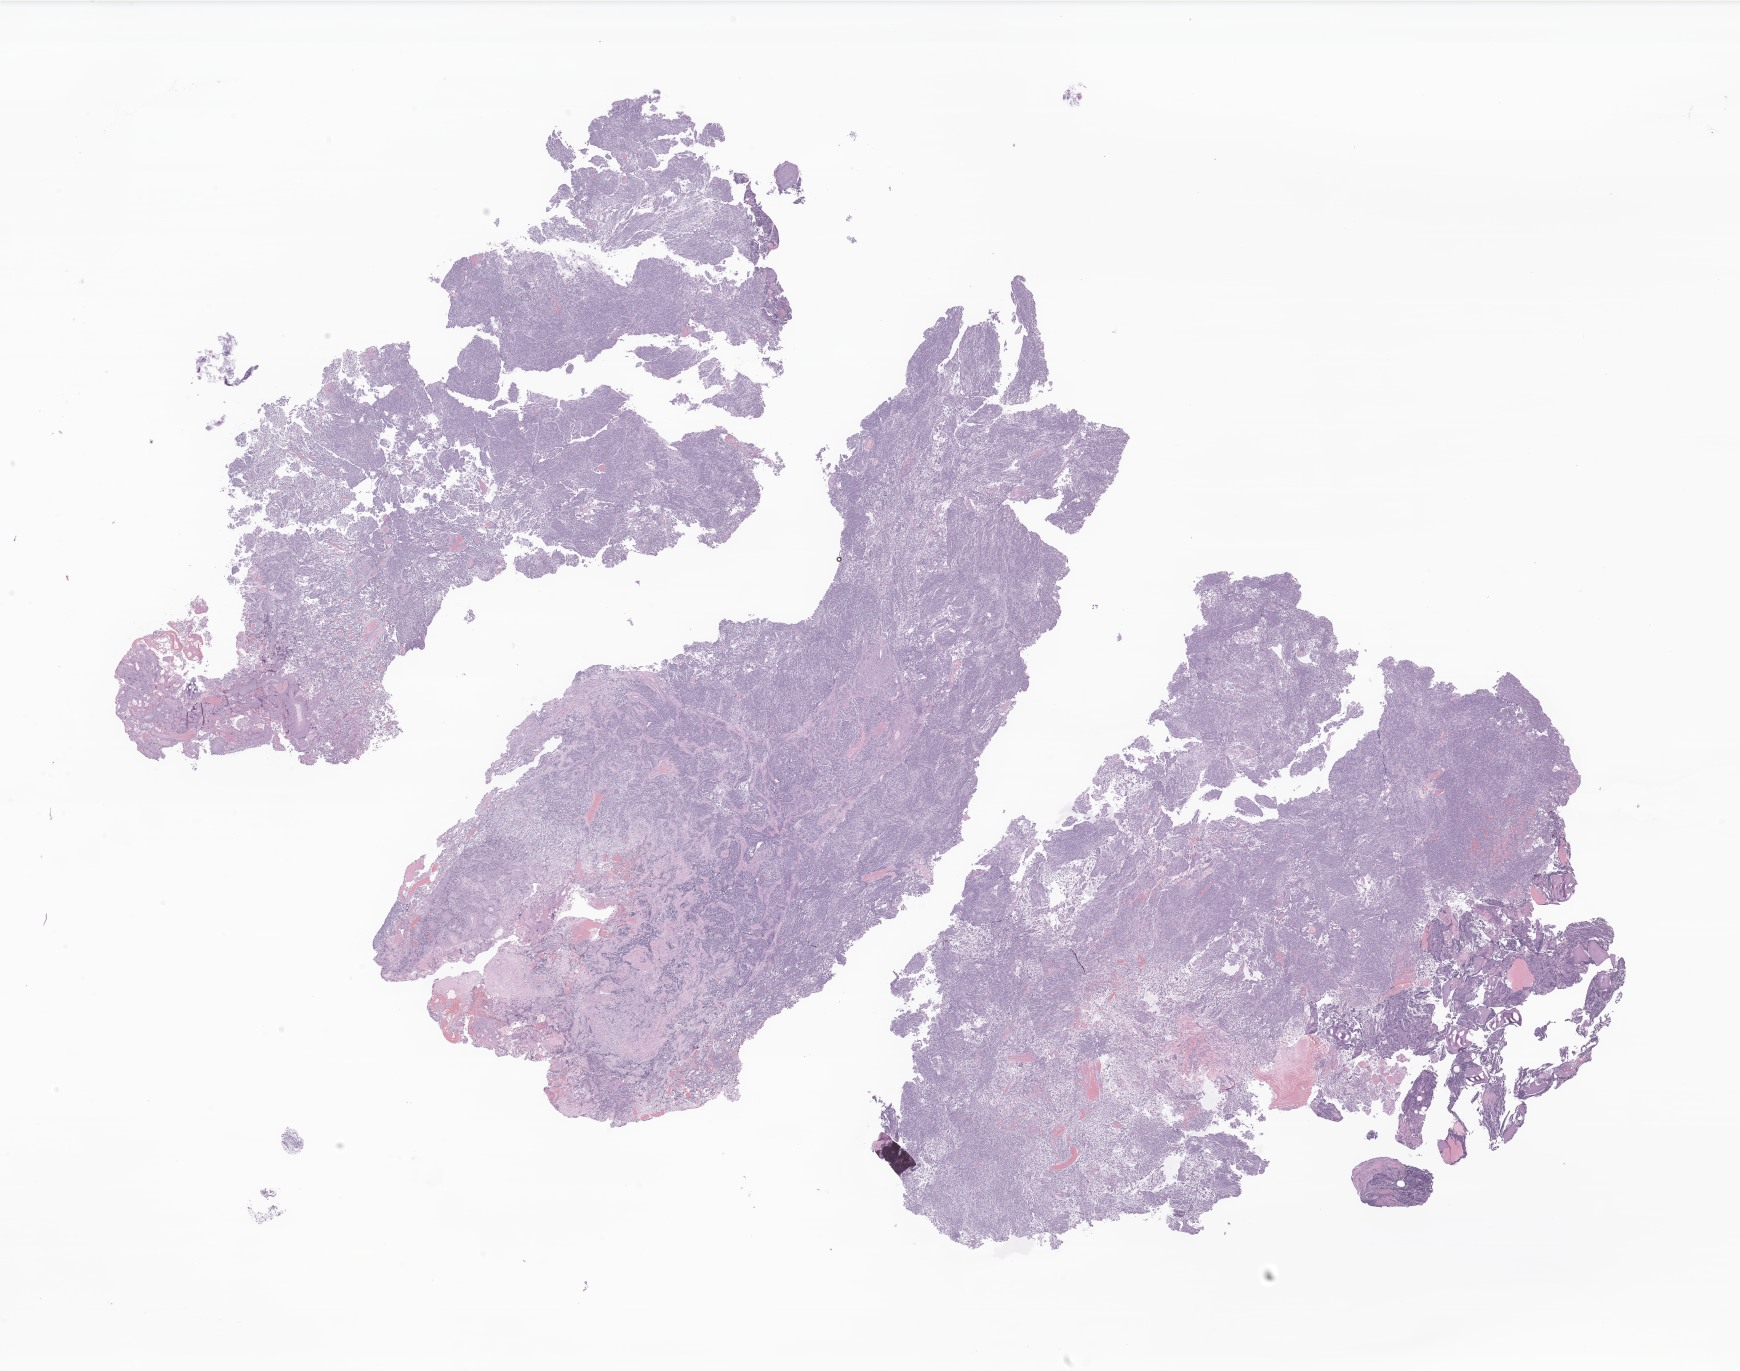
Haematoxylin and eosin whole-slide image of tumor tissue from the brain — shown as a low-resolution overview of the whole scanned area (about 29.3 x 23.1 mm). Formalin-fixed, paraffin-embedded (FFPE) tissue. Patient: male, age 83 months.
Diagnosis (ICD-O-3 morphology term): Medulloblastoma, NOS.